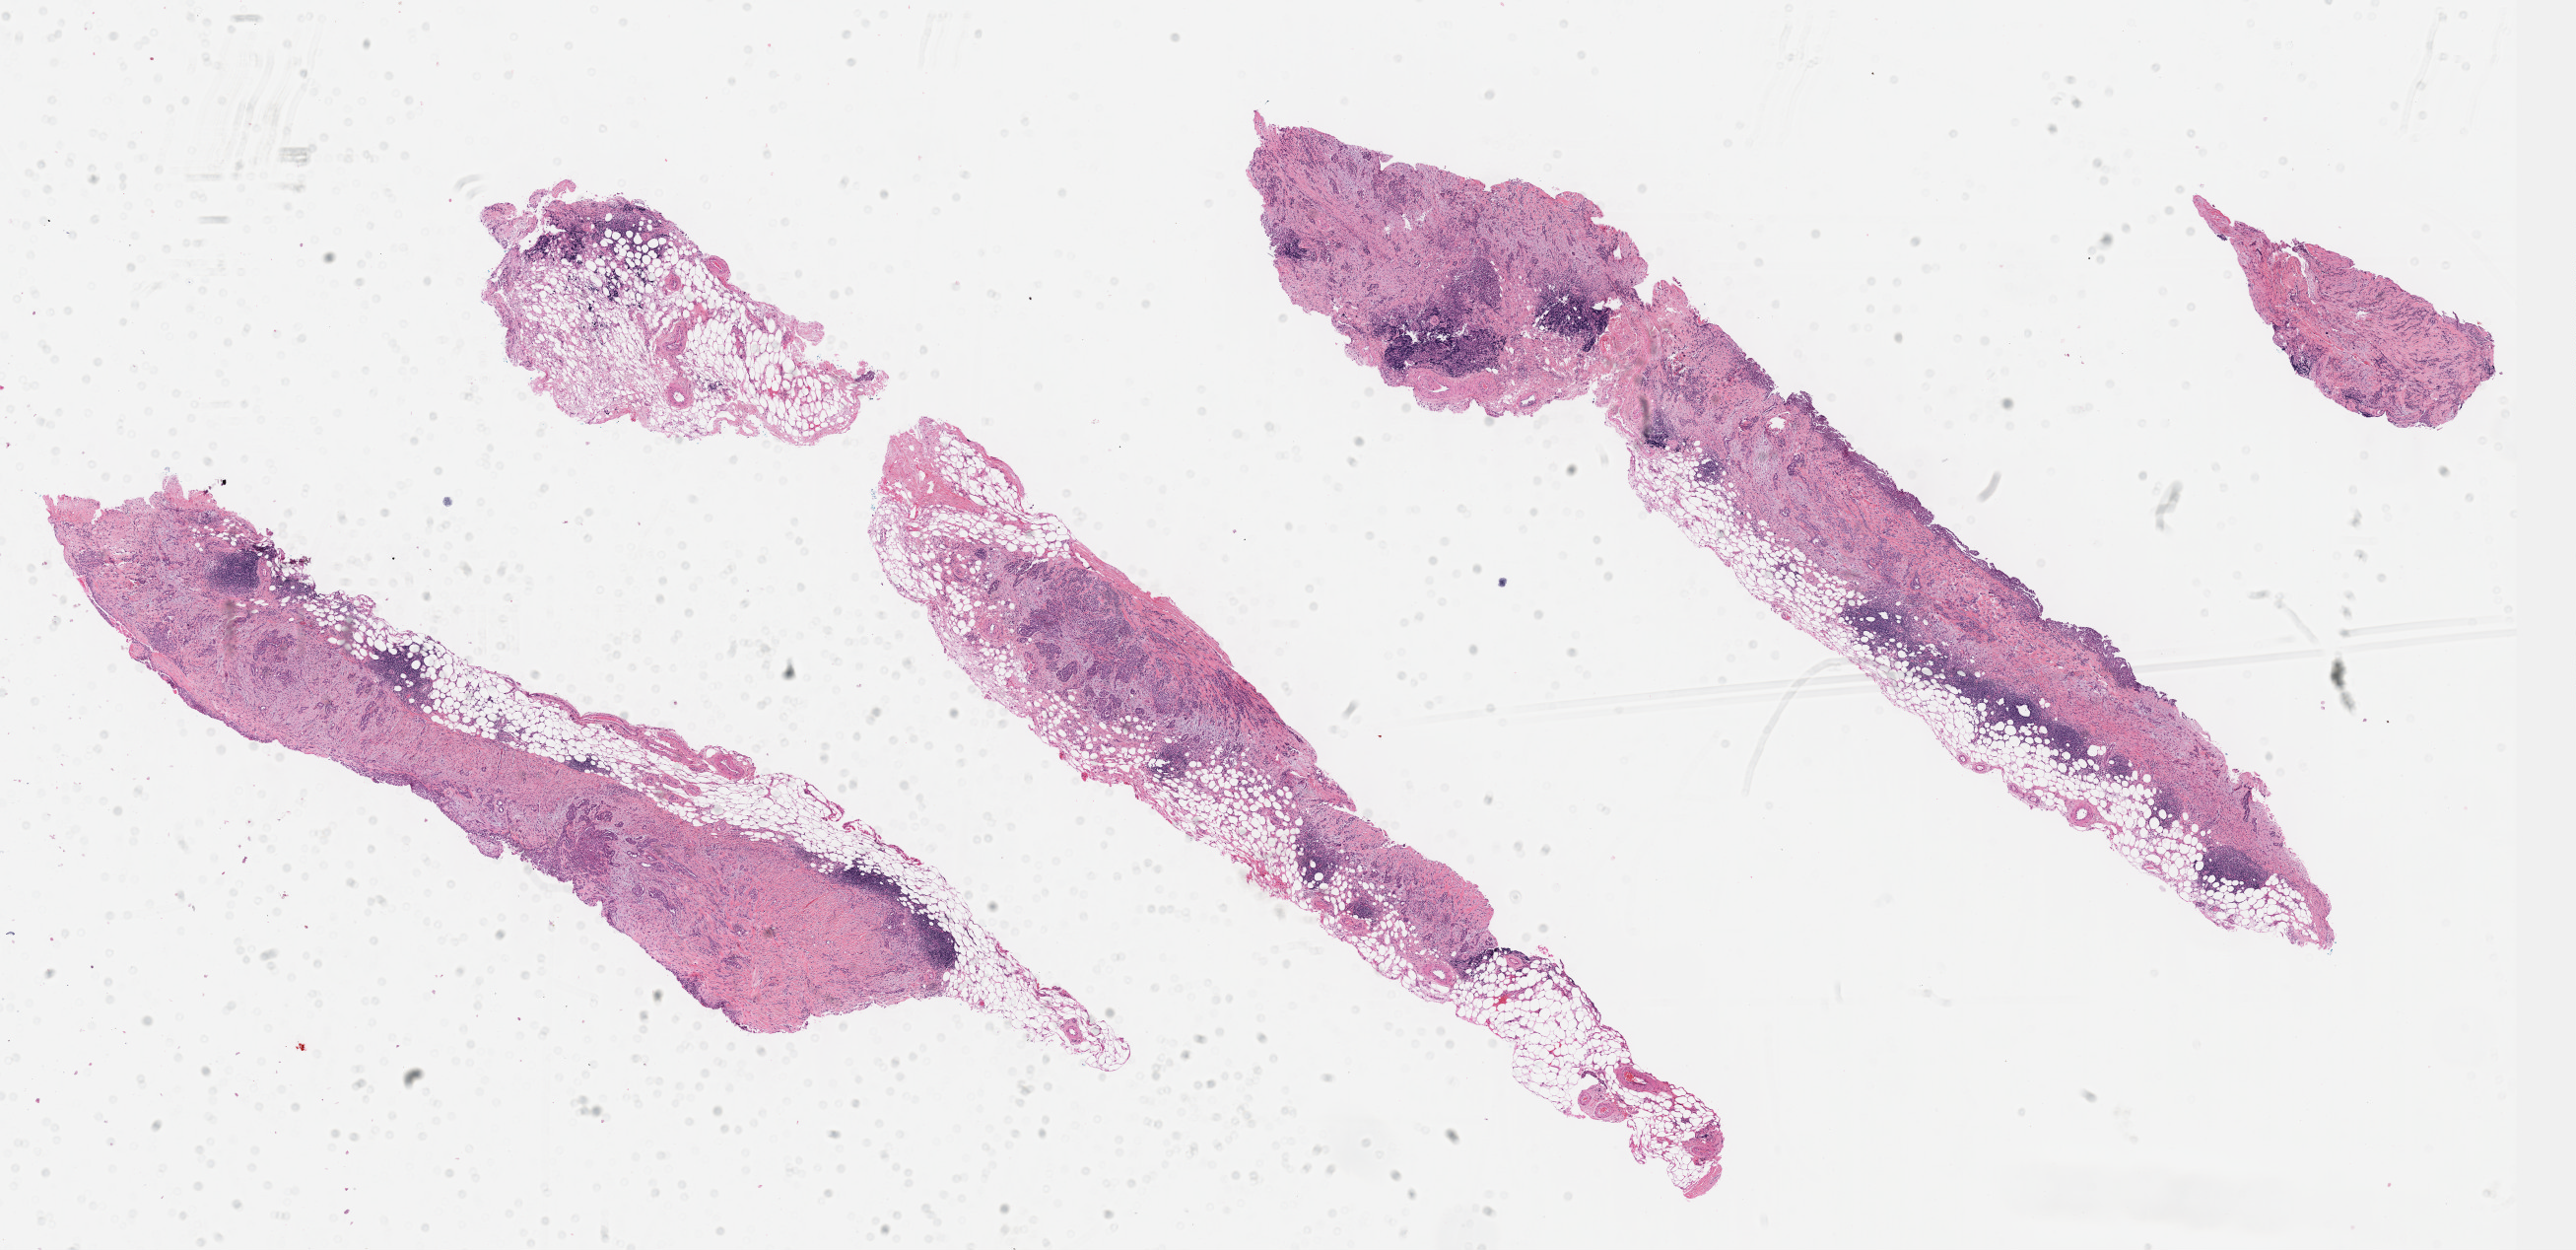
Digitized Hematoxylin and eosin (H&E) stained tissue section (whole slide) — shown as a low-resolution overview of the whole scanned area (about 21.1 x 10.2 mm, acquisition: 40x scan); formalin-fixed paraffin-embedded (FFPE) diagnostic section; mesothelium, primary tumour sample. Male, age 66 years at initial diagnosis.
* AJCC pathologic stage: II (7th edition)
* histologic diagnosis: Epithelioid mesothelioma, malignant (pleura, NOS)